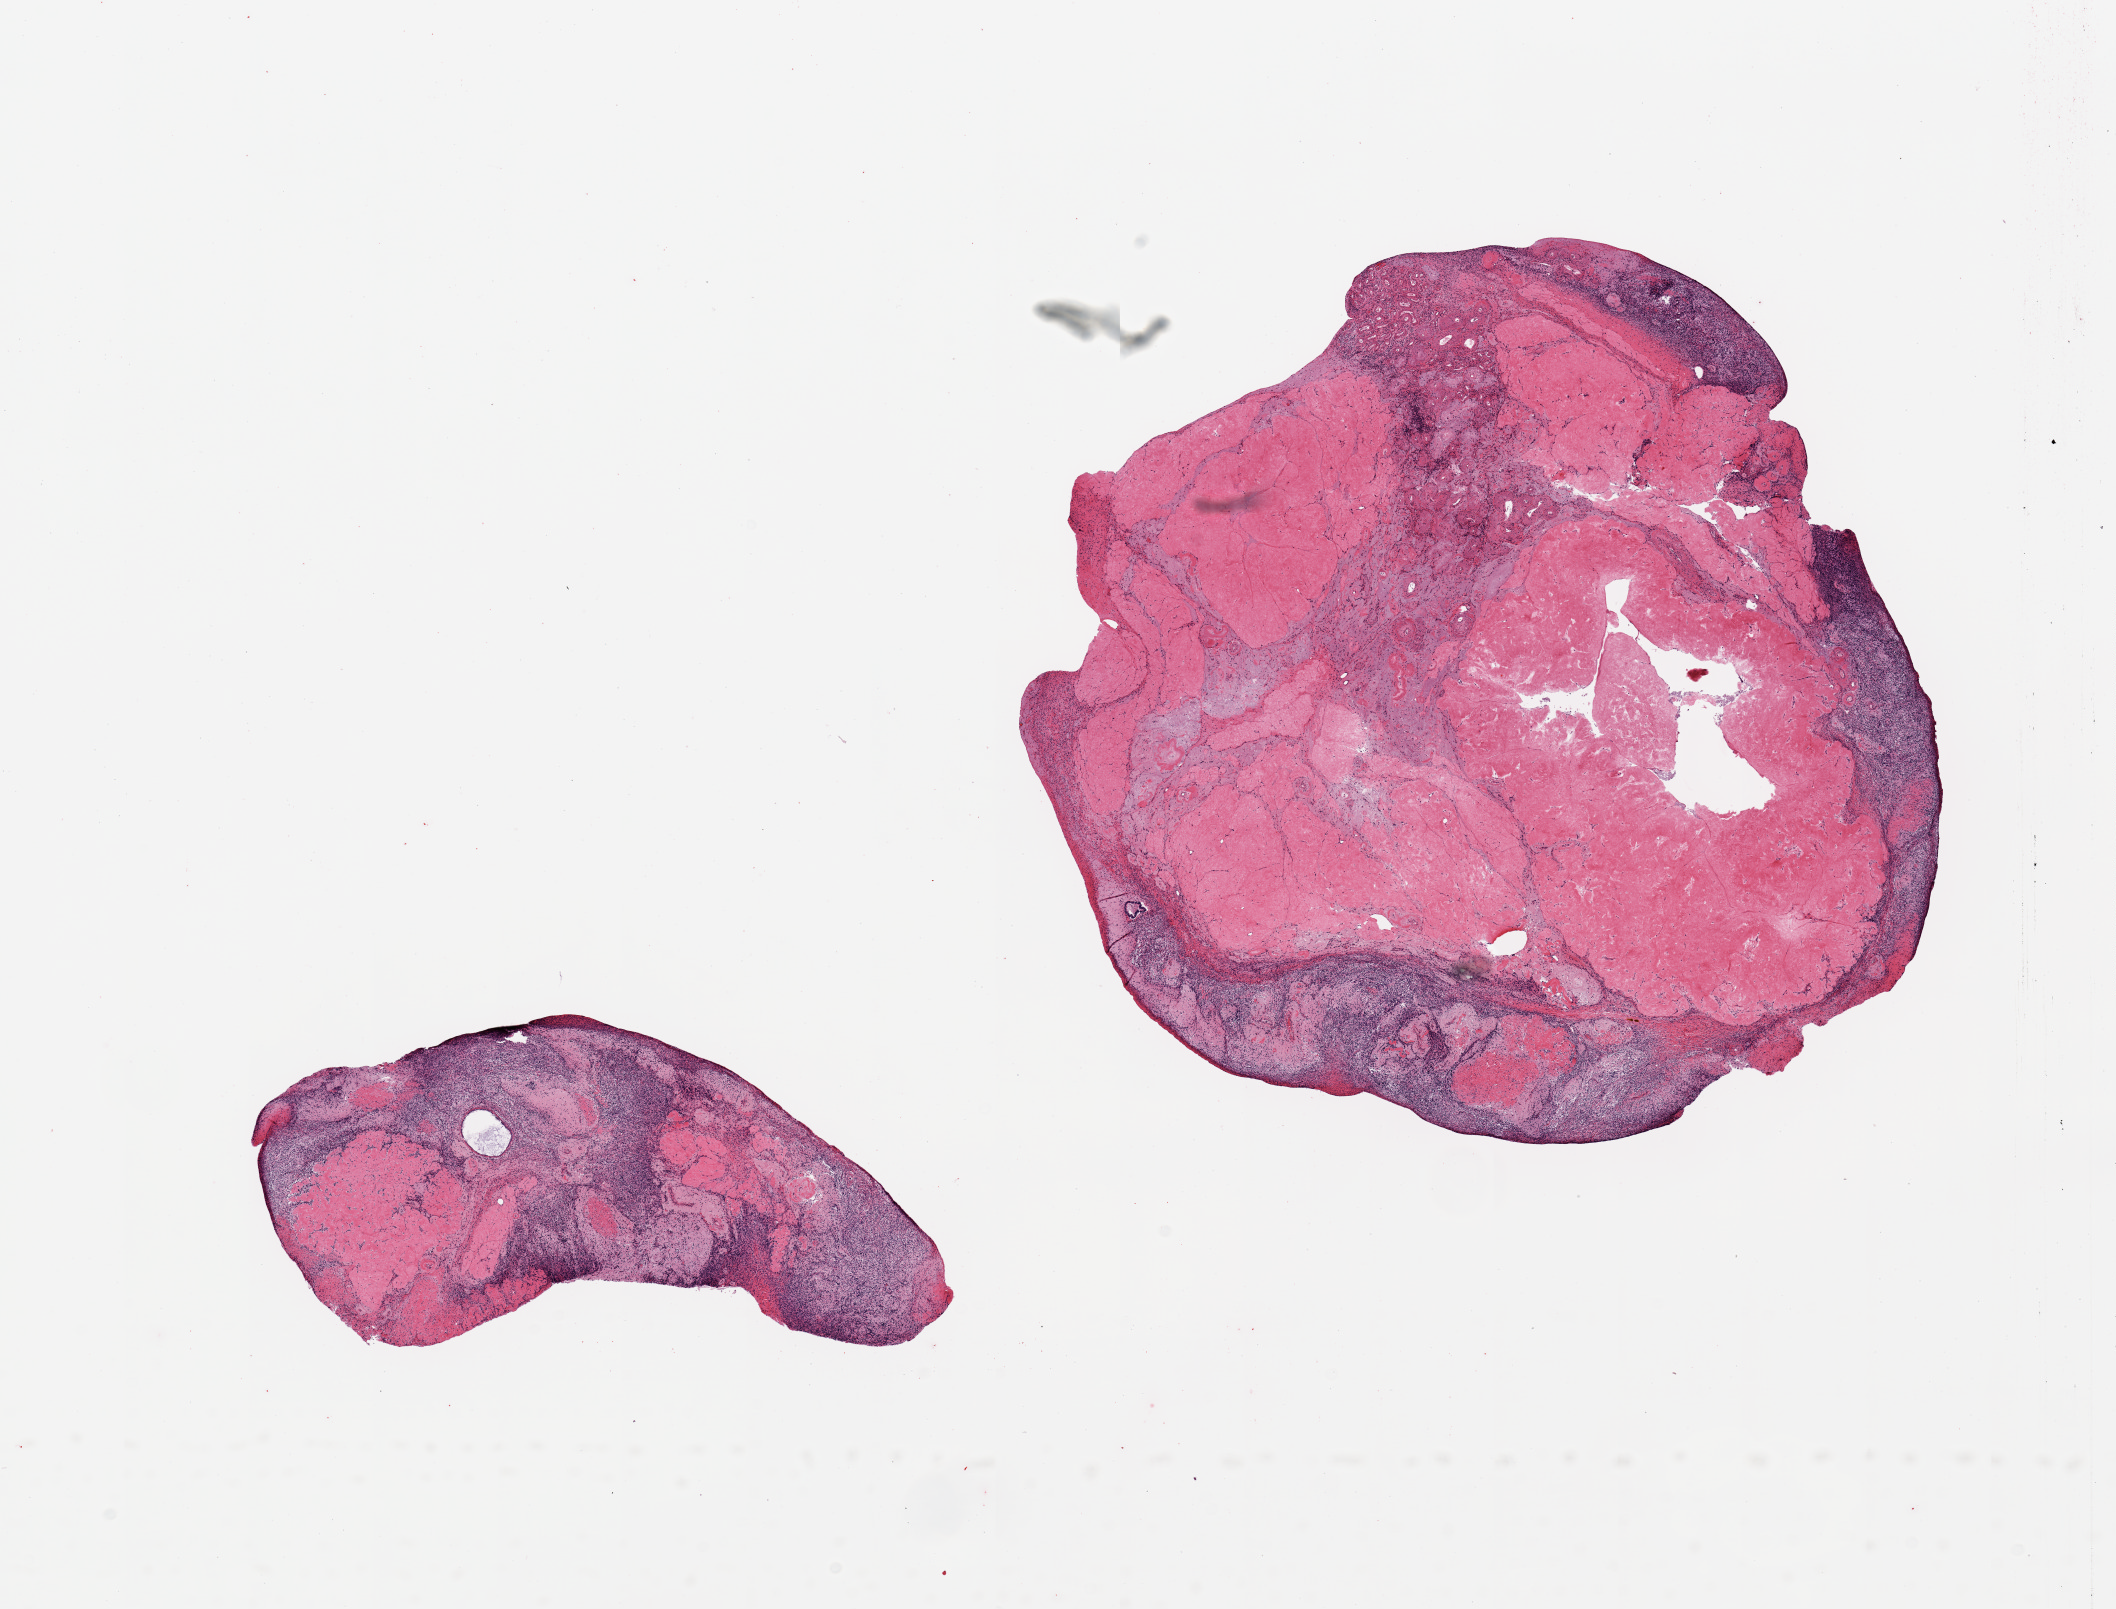
Digitized hematoxylin and eosin (H&E)-stained section, brightfield, shown as a low-resolution overview of the whole scanned area (about 16.7 x 12.7 mm, from a 20x scan); PAXgene-fixed paraffin-embedded (PFPE) section; section of ovary (target tissue); tissue donor sample. Donor: female.
• pathologist's review note for this sample: 2 pieces